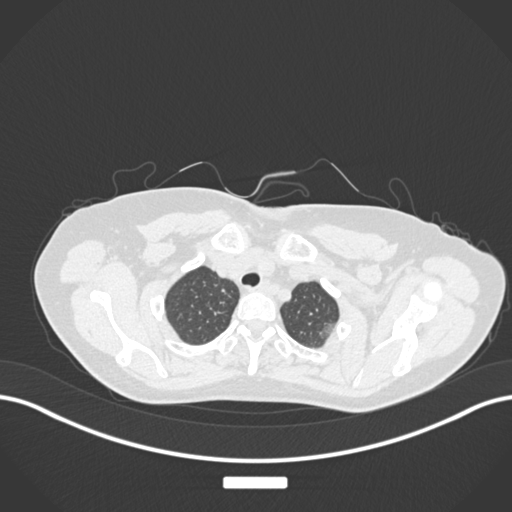
Chest CT, one axial slice. Slice 154 of 181 in the series (ordered by position). Reconstruction kernel B30f. 120 kVp. Lung window (W 1500 / L -600 HU). 512 × 512 image matrix, field of view 400 × 400 mm. Female patient, age 58 years. Case-level facts recorded for this patient, not image findings: clinical TNM (as recorded): T1c N0 M0.
Outlined on this slice (rectangle marked by the reading radiologist):
- lung tumour (recorded histology: adenocarcinoma): bounding box [x1, y1, x2, y2] px = [314, 317, 338, 346]